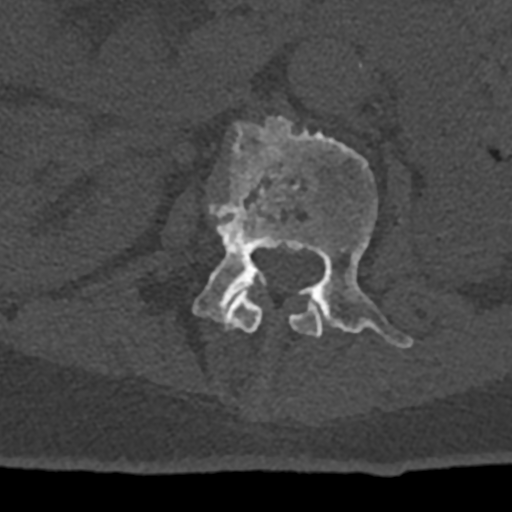
CT including the spine, one axial slice. Position 396 of 797 along the scan axis. Reconstruction kernel Br40s/3. Bone window (W 1800 / L 400 HU). 0.5 mm slice thickness. 512 × 512 image matrix, field of view 160 × 160 mm. Male patient, age 74 years. Case-level facts recorded for this patient, not image findings: primary cancer: renal; vertebrae with lytic lesions (as recorded): T10, L1, L2, L3, L4, L5.
Structures marked on this image (semi-automatic segmentation, software-assisted and operator-edited):
- L1 vertebra: bounding box [x1, y1, x2, y2] px = [209, 203, 322, 337]
- L2 vertebra: [193, 116, 413, 349]